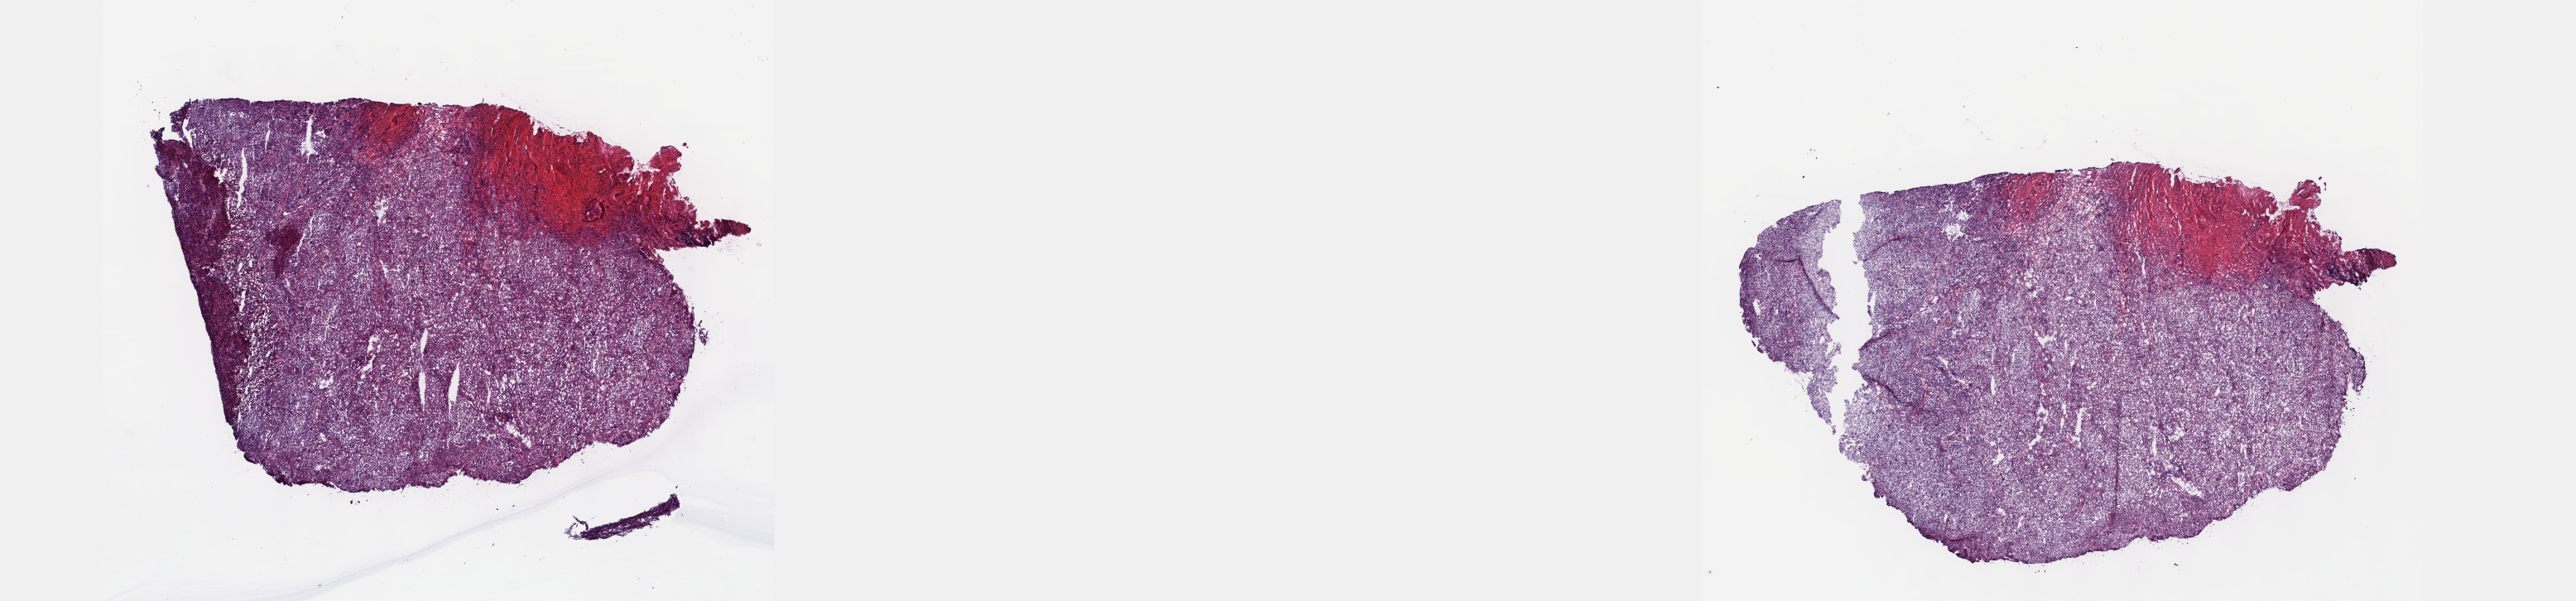
H&E whole-slide image, low-resolution overview of the scanned area, about 25.1 x 5.9 mm (acquisition: 40x scan); frozen section; primary tumour sample from the cervix. Female, age 79 years at initial diagnosis. Histologic grade: G2 (moderately differentiated). Pathologist review of this section (percent, as recorded): tumour cells 80%, tumour nuclei 80%, normal cells 0%, stromal cells 15%, necrosis 5%. Infiltration values recorded for this section: lymphocyte infiltration 40%, monocyte infiltration 20%, neutrophil infiltration 20%.
• pathologic diagnosis: Squamous cell carcinoma, NOS (cervix uteri)
• FIGO stage: IB1